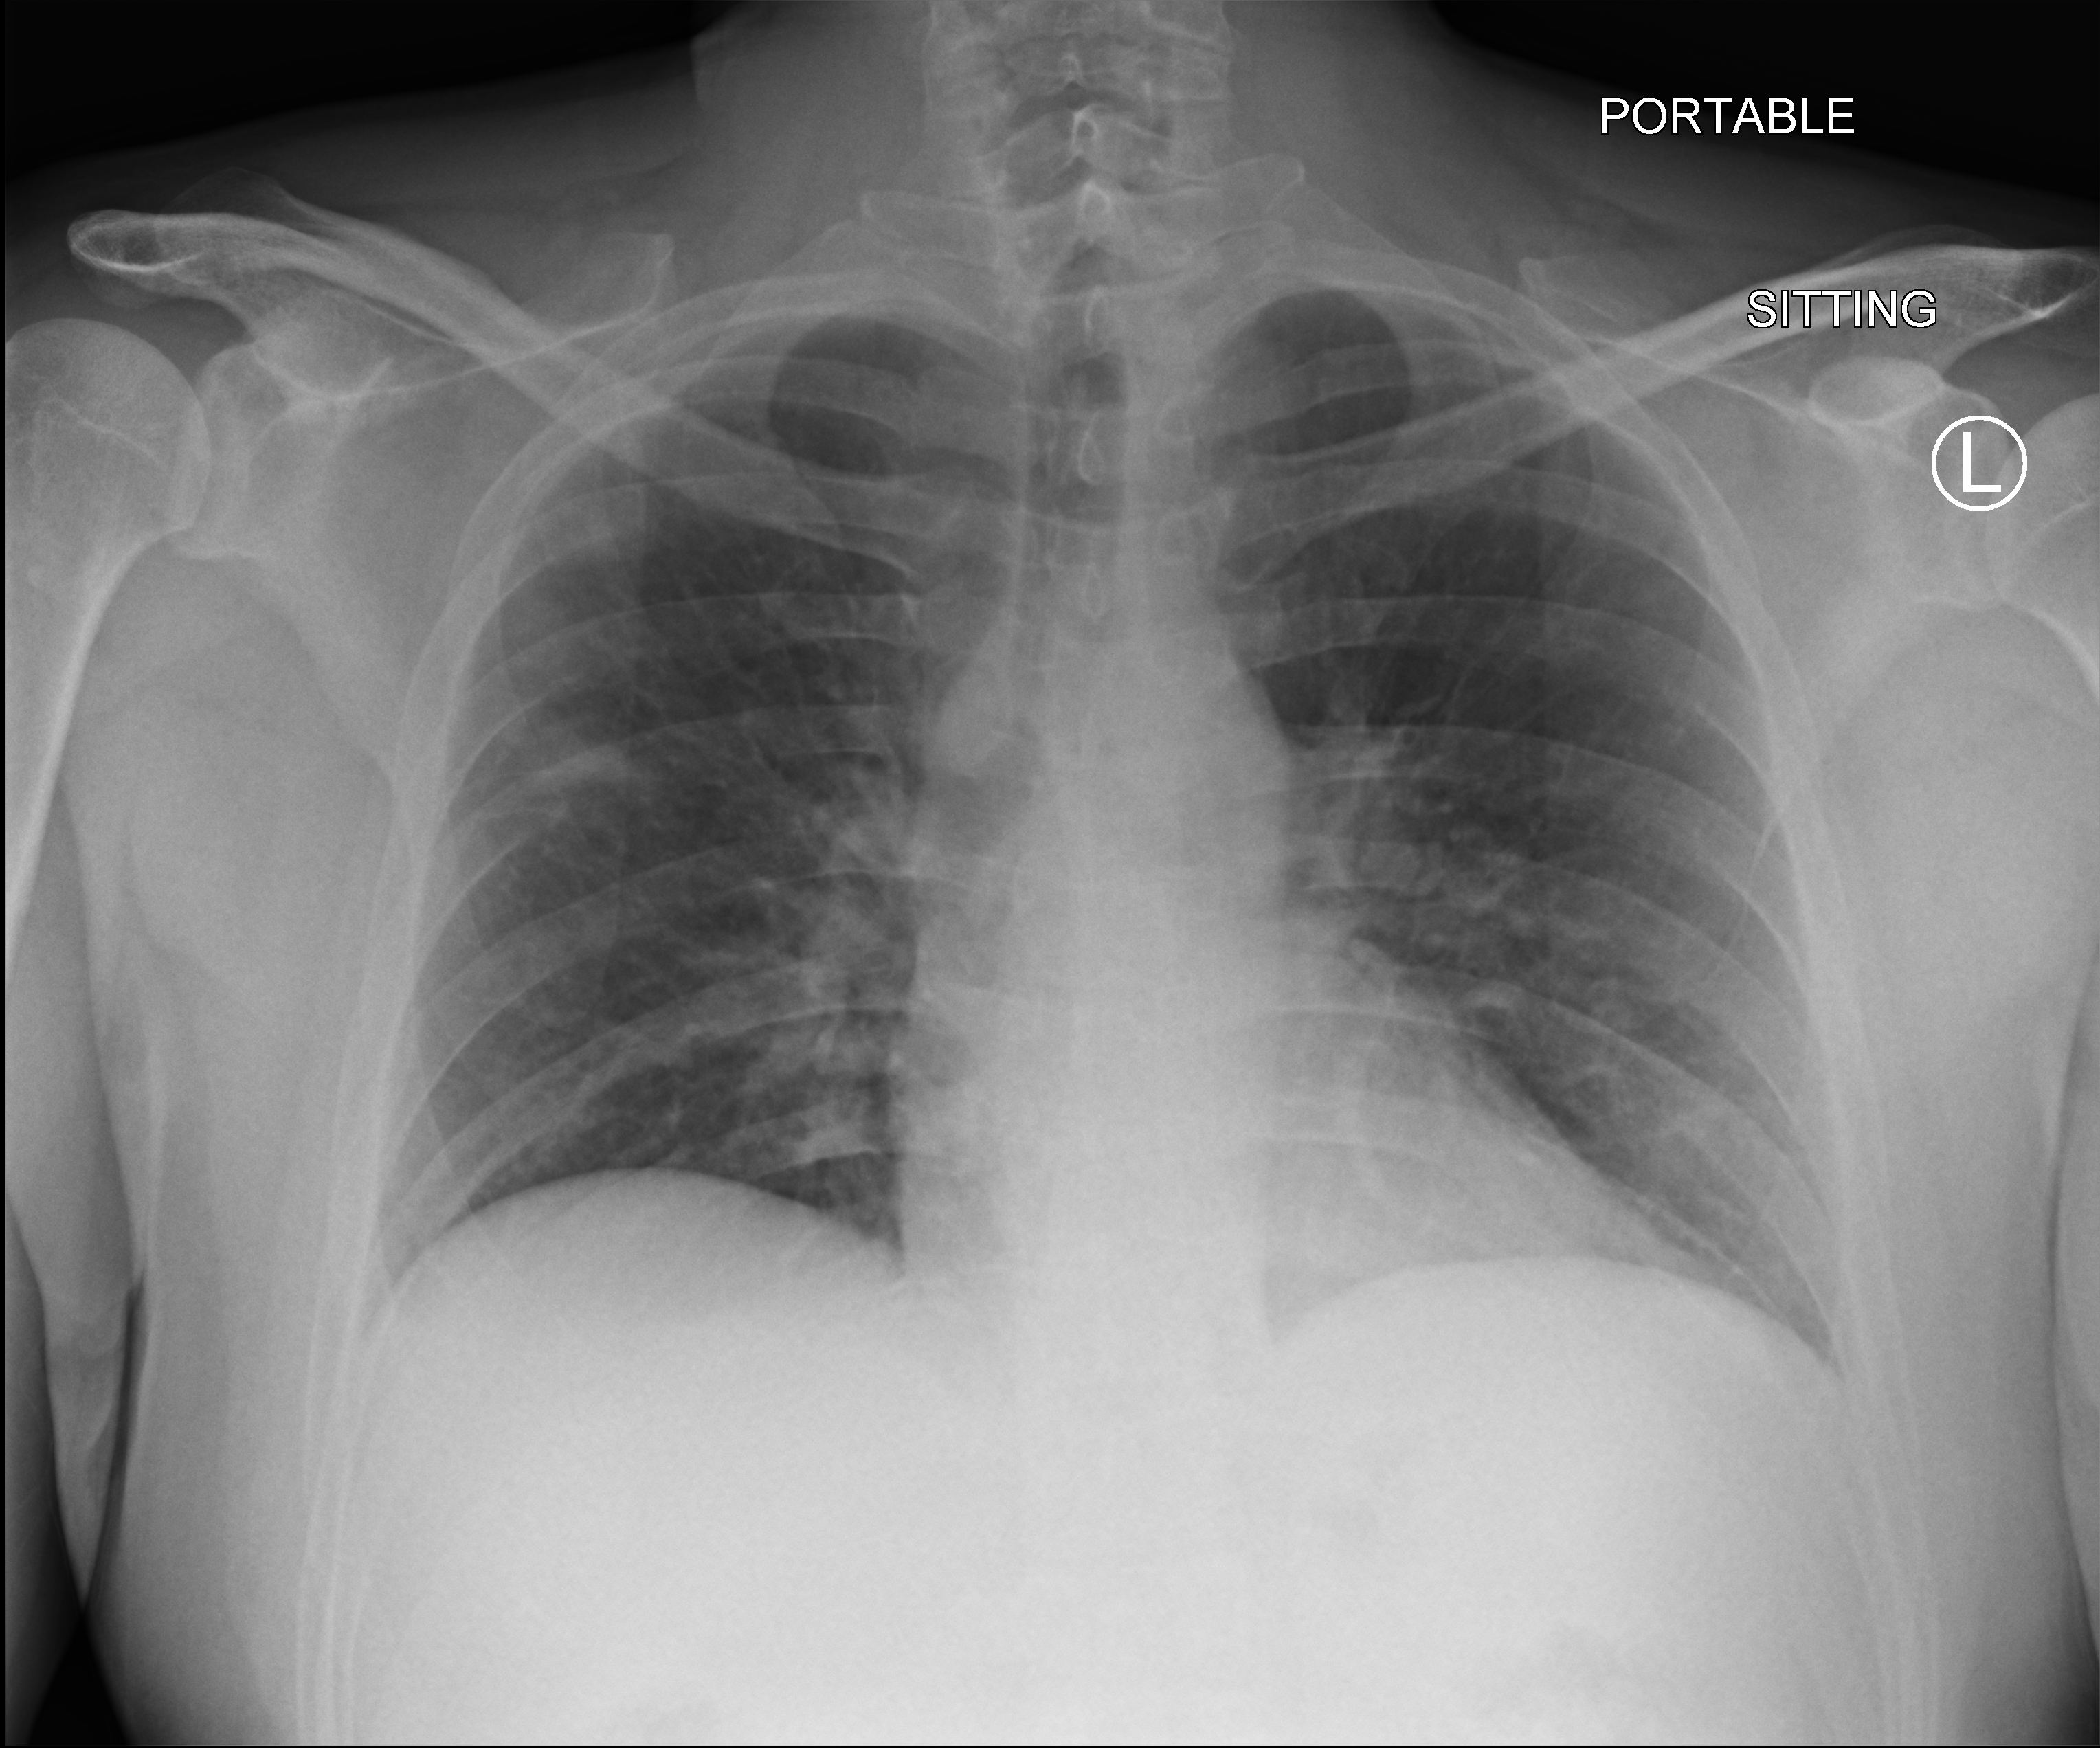
Portable chest radiograph, anteroposterior (AP) projection. Patient hospitalised with COVID-19; male, aged 18–59 years.
Hospital-stay facts (about this admission, not read from this image; timing relative to this image not recorded):
- length of hospital stay: 7 days
- admitted to intensive care during this hospital stay: no